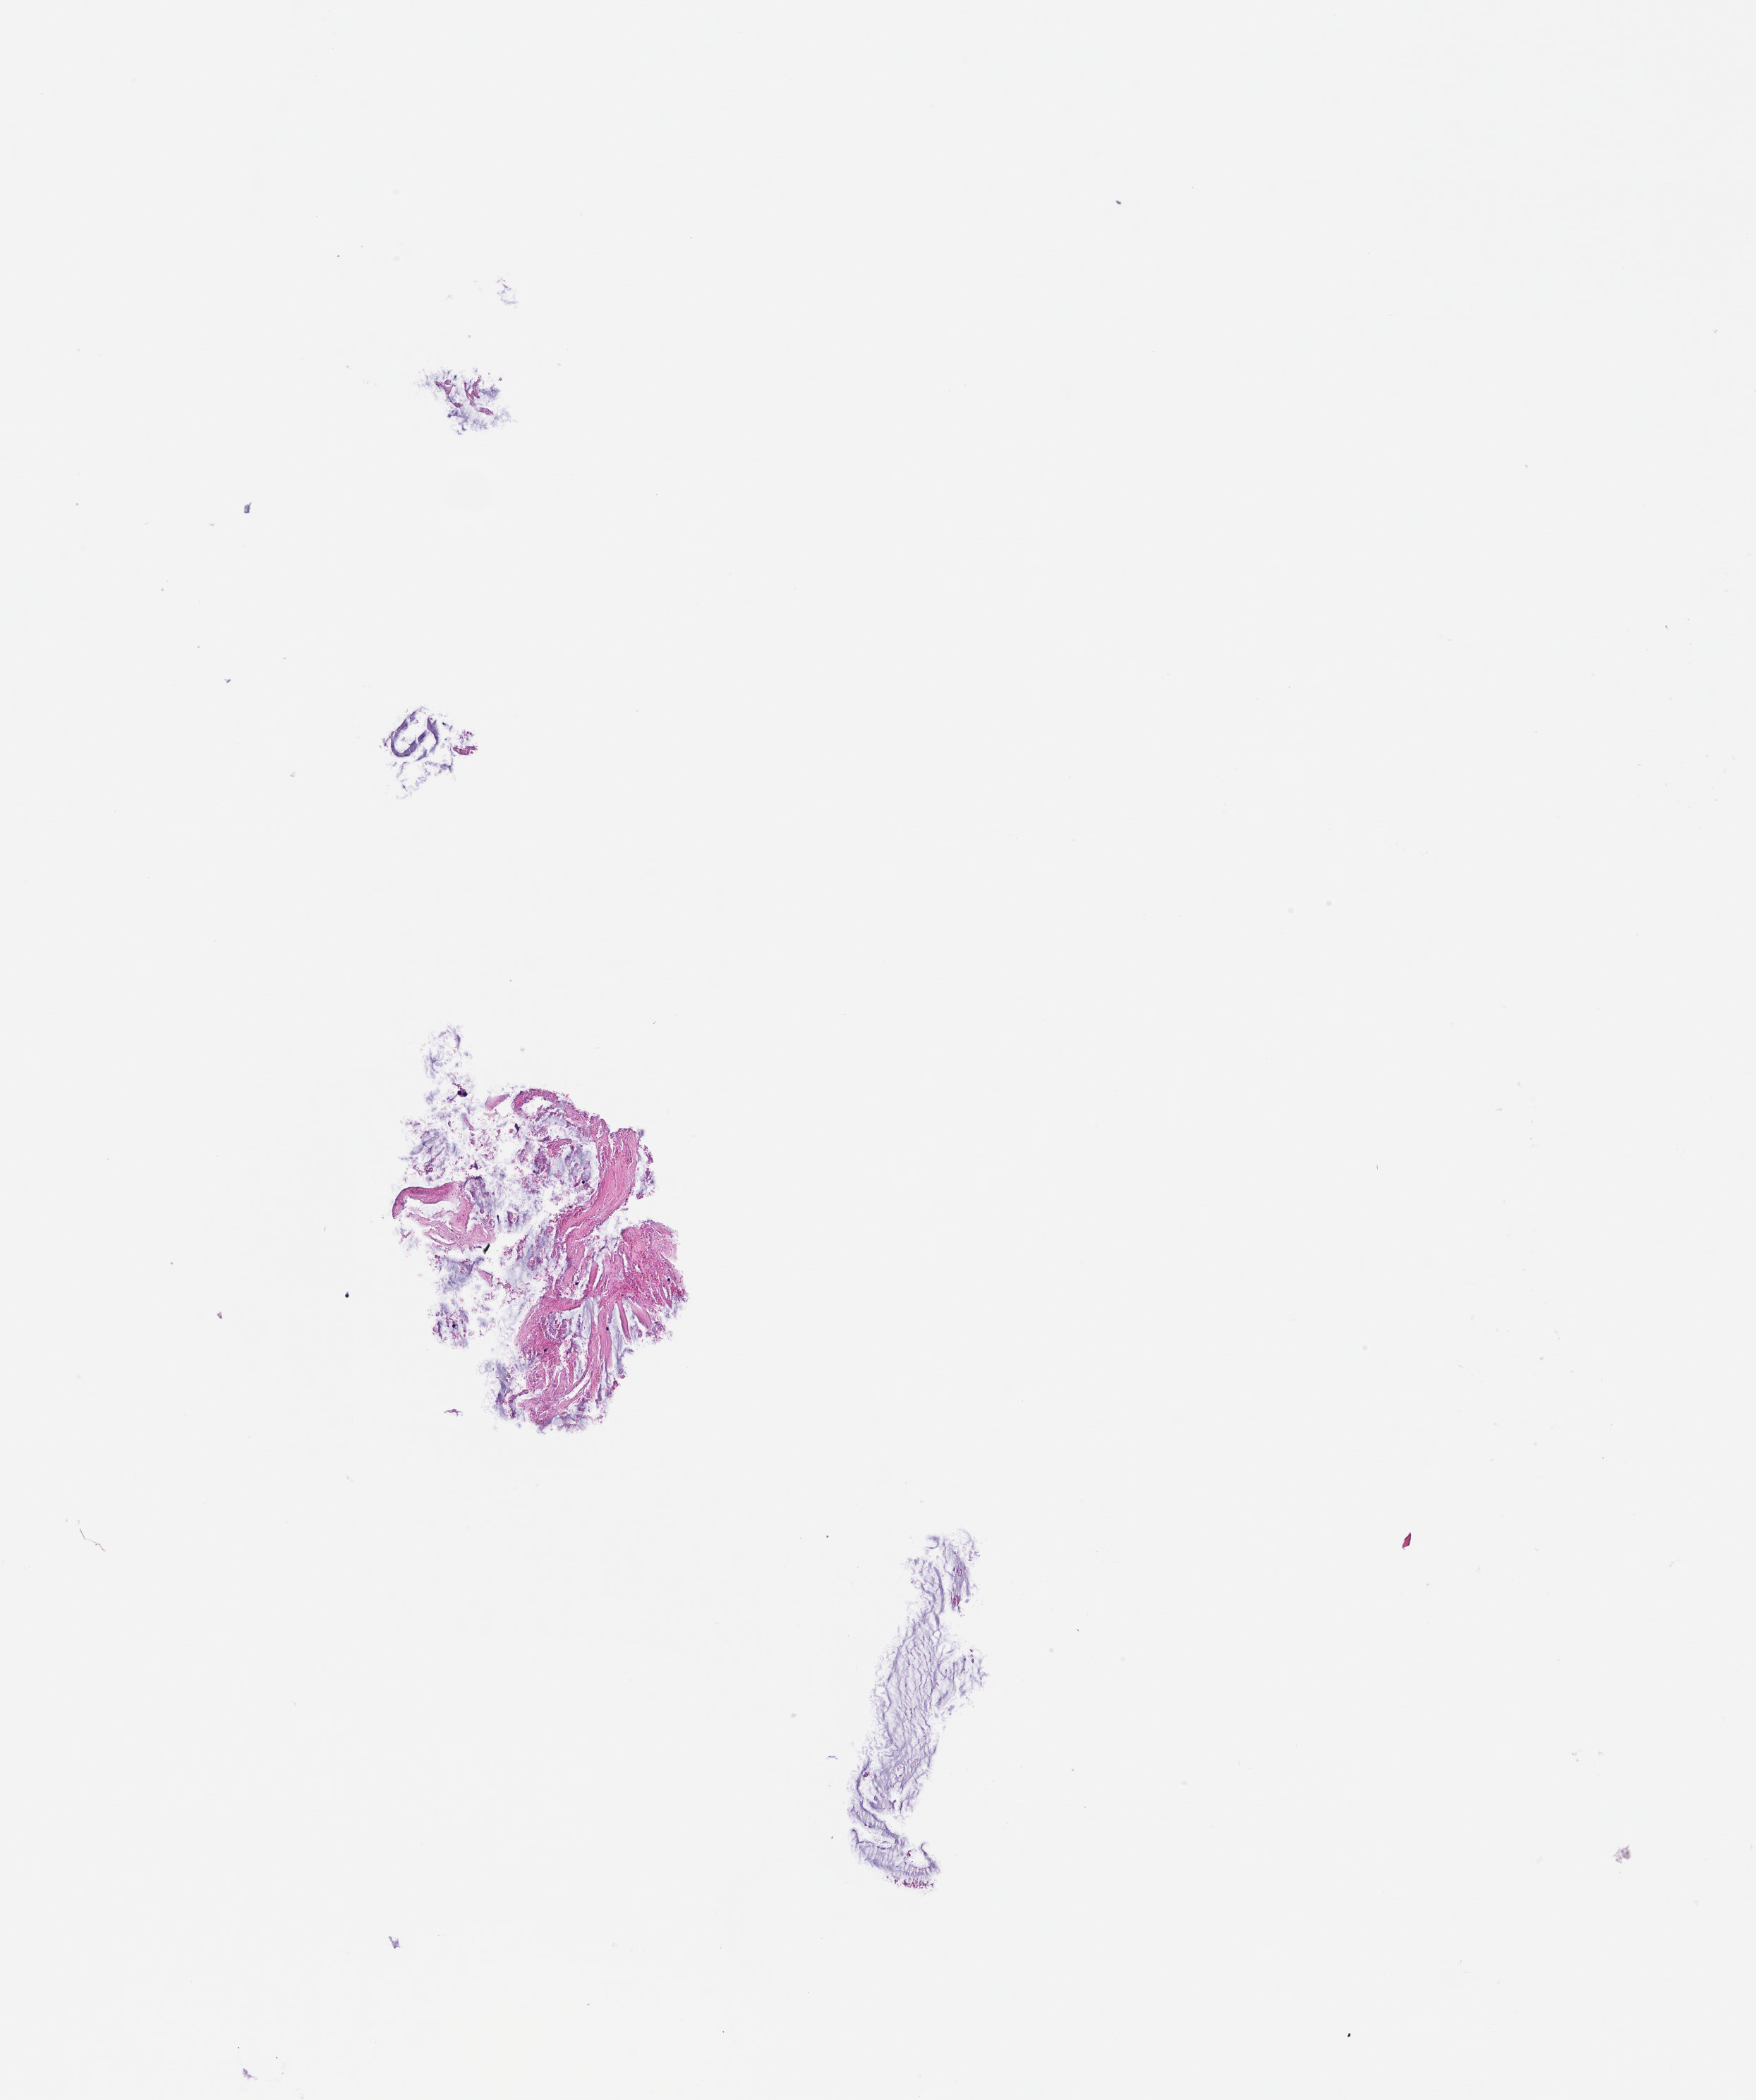
Digitized haematoxylin and eosin-stained section — shown as a low-resolution overview of the whole scanned area (about 2.5 x 3.0 mm). Formalin-fixed paraffin-embedded section. Patient sex: male.
This section: metastasis (sampled organ not recorded). Patient diagnosis (primary): Colorectal Carcinoma.